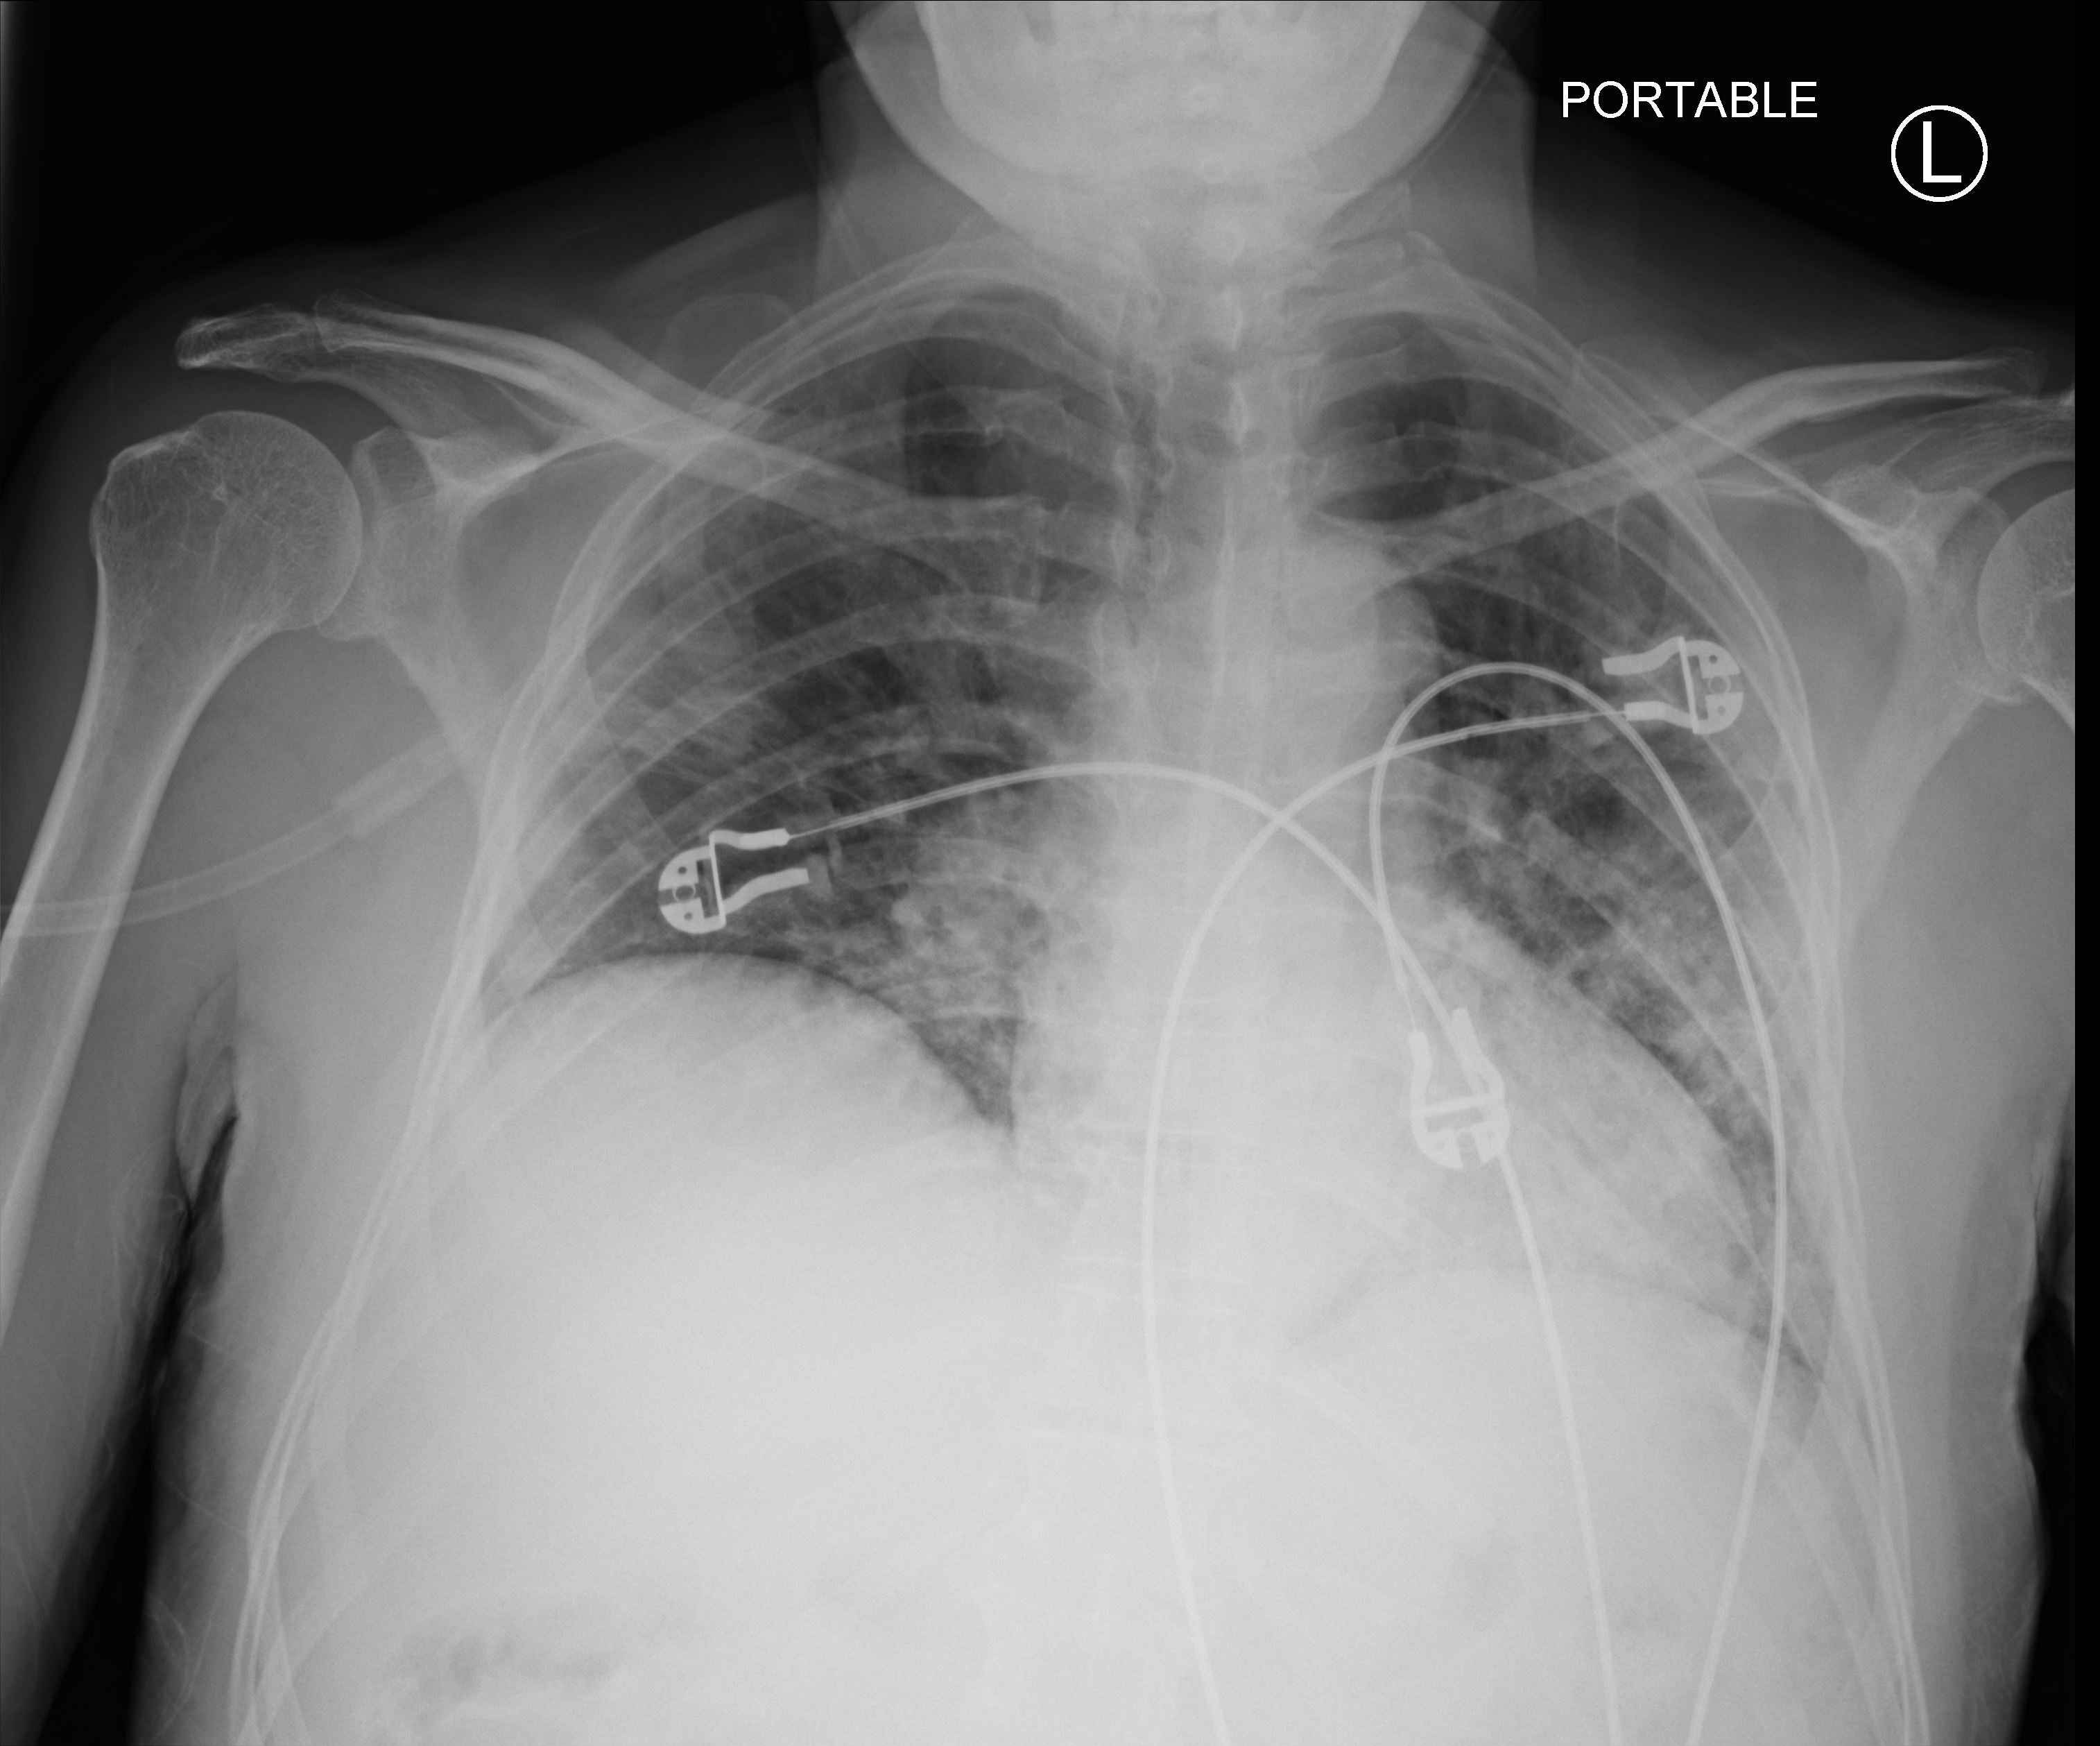
Bedside chest radiograph (computed radiography). Patient hospitalised with COVID-19; male, aged 60–74 years.
Admission-level facts for this patient (not findings on this image; timing relative to this image not recorded):
- smoking status (admission record): never
- mechanically ventilated during this hospital stay: no
- admitted to intensive care during this hospital stay: no